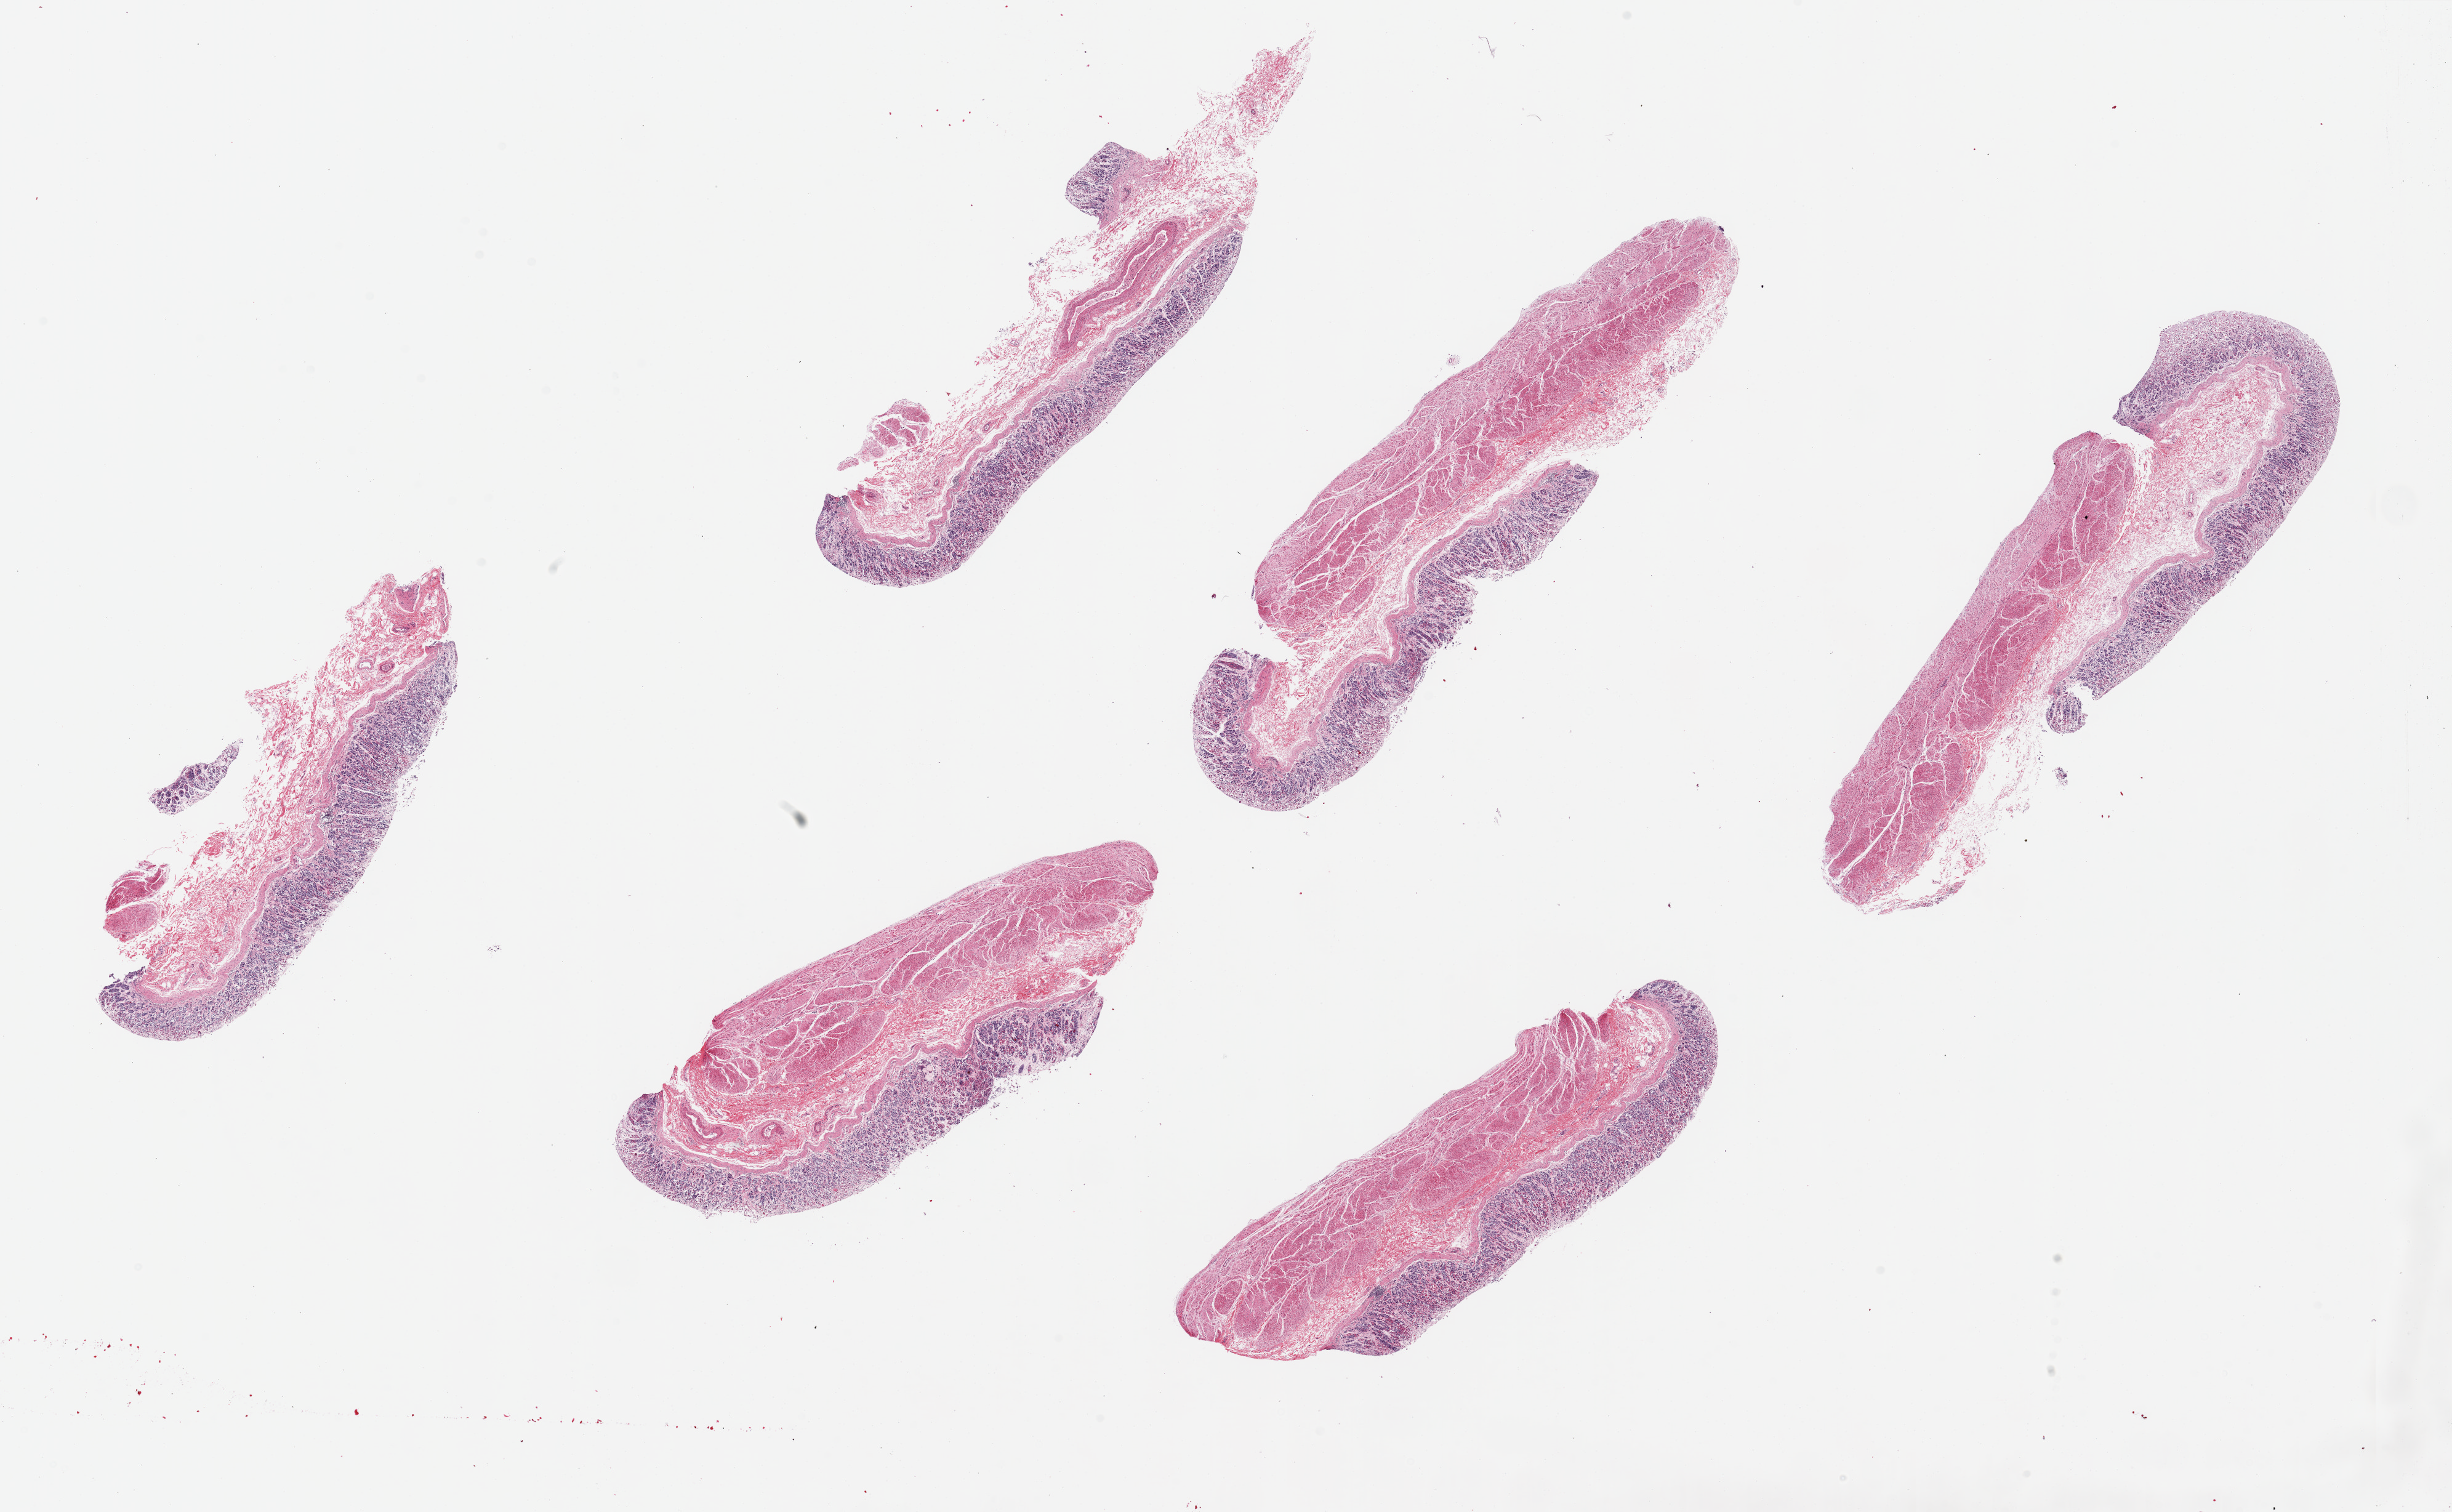
H&E whole-slide image, brightfield — low-resolution overview of the scanned area, about 31.5 x 19.4 mm; PAXgene-fixed paraffin-embedded (PFPE) section; sampled site (target tissue): stomach; tissue donor sample. Donor sex: male.
- reviewer comment on this tissue sample: 6 pieces, up to 10x3mm; mucosa autolysis= 2 and 3; muscularis = 2